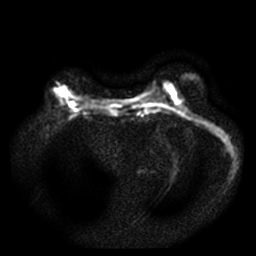
Breast MRI, one axial slice; position 15 of 49 along the scan axis; diffusion-weighted series; image 2 of 4 stored at this slice position (different b-values; order by instance number); 3 T; 5 mm slice thickness; 256 × 256 image matrix, field of view 340 × 340 mm. Female patient.
Structures marked on this image (manually delineated by an expert):
- tumour on diffusion-weighted imaging: bounding box <59,89,69,96> (left, top, right, bottom; pixels)